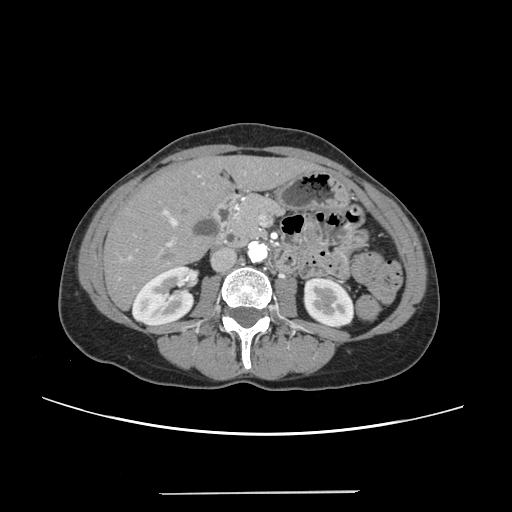
Contrast-enhanced abdominal CT, one axial slice; position 101 of 240 along the scan axis; intravenous contrast given; soft-tissue window (W 400 / L 40 HU); 1.25 mm slice thickness; 512 × 512 image matrix, field of view 371 × 371 mm. Female patient, age 60 years. From the clinical record (not read from this slice): diagnosis: colorectal cancer liver metastases, imaged before liver resection; multiple liver metastases: no; largest metastasis: 1.5 cm.
Annotated regions visible in this slice (manually delineated by an expert):
- liver: bounding box (x1, y1, x2, y2) in pixels: (105, 157, 309, 308)
- planned liver remnant (the part of the liver to remain after resection): (105, 158, 311, 308)
- portal vein (with intrahepatic branches): (121, 174, 200, 260)